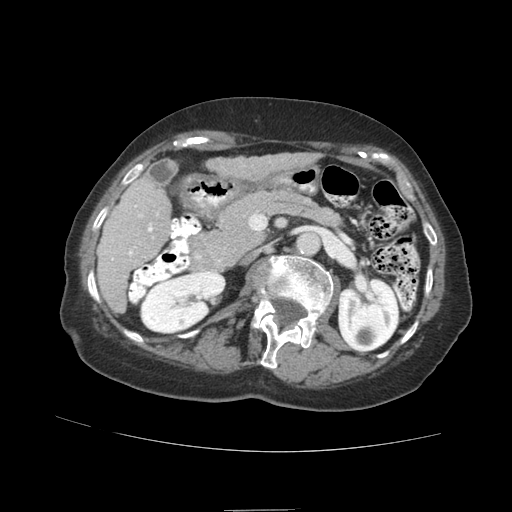
Contrast-enhanced abdominal CT (liver protocol), one axial slice. Slice 34 of 89 in the series (ordered by position). Soft-tissue window (W 400 / L 40 HU). 2.5 mm slice thickness. 512 × 512 image matrix. From the clinical record (not read from this slice): diagnosis: hepatocellular carcinoma (patient treated with transarterial chemoembolisation; whether this scan precedes or follows treatment is not stated here); TNM stage (as recorded): Stage-II; Child-Pugh class: A; tumour differentiation: moderately differentiated.
Structures marked on this image (semi-automatically segmented with operator editing):
- liver parenchyma outside the tumour (the mass and vessels are separate outlines, so this box may not span the whole liver): bounding box <98,152,318,312> (left, top, right, bottom; pixels)
- liver vessels: <111,205,158,260>